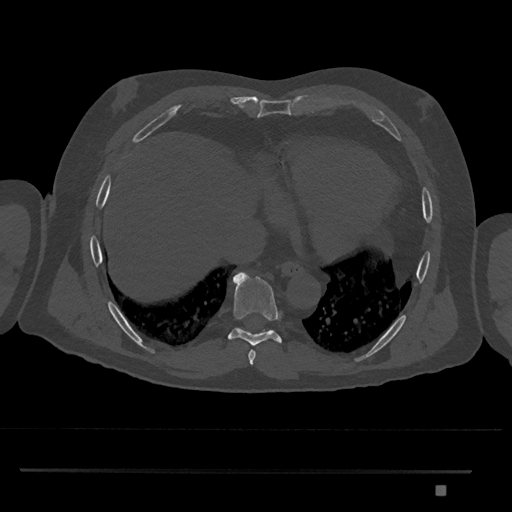
CT including the spine, one axial slice. Slice 1106 of 1134 in the series (ordered by position). Bone window (W 1800 / L 400 HU). 0.5 mm slice thickness. 512 × 512 image matrix. Male patient, age 65 years. From the clinical record (not read from this slice): primary cancer: prostate.
Outlined on this slice (semi-automatically segmented with operator editing):
- T8 vertebra: bounding box <228,271,282,346> (left, top, right, bottom; pixels)